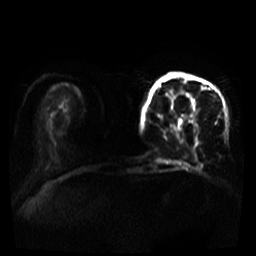
Breast MRI, one axial slice; slice 10 of 39 in the series (ordered by position); diffusion-weighted series; image 2 of 4 stored at this slice position (different b-values; order by instance number); 3 T; 5 mm slice thickness; 256 × 256 image matrix, field of view 320 × 320 mm. Female patient.
Structures marked on this image (outlined manually by an expert reader):
- tumour on diffusion-weighted imaging: box from (x=185, y=93) to (x=192, y=117) px